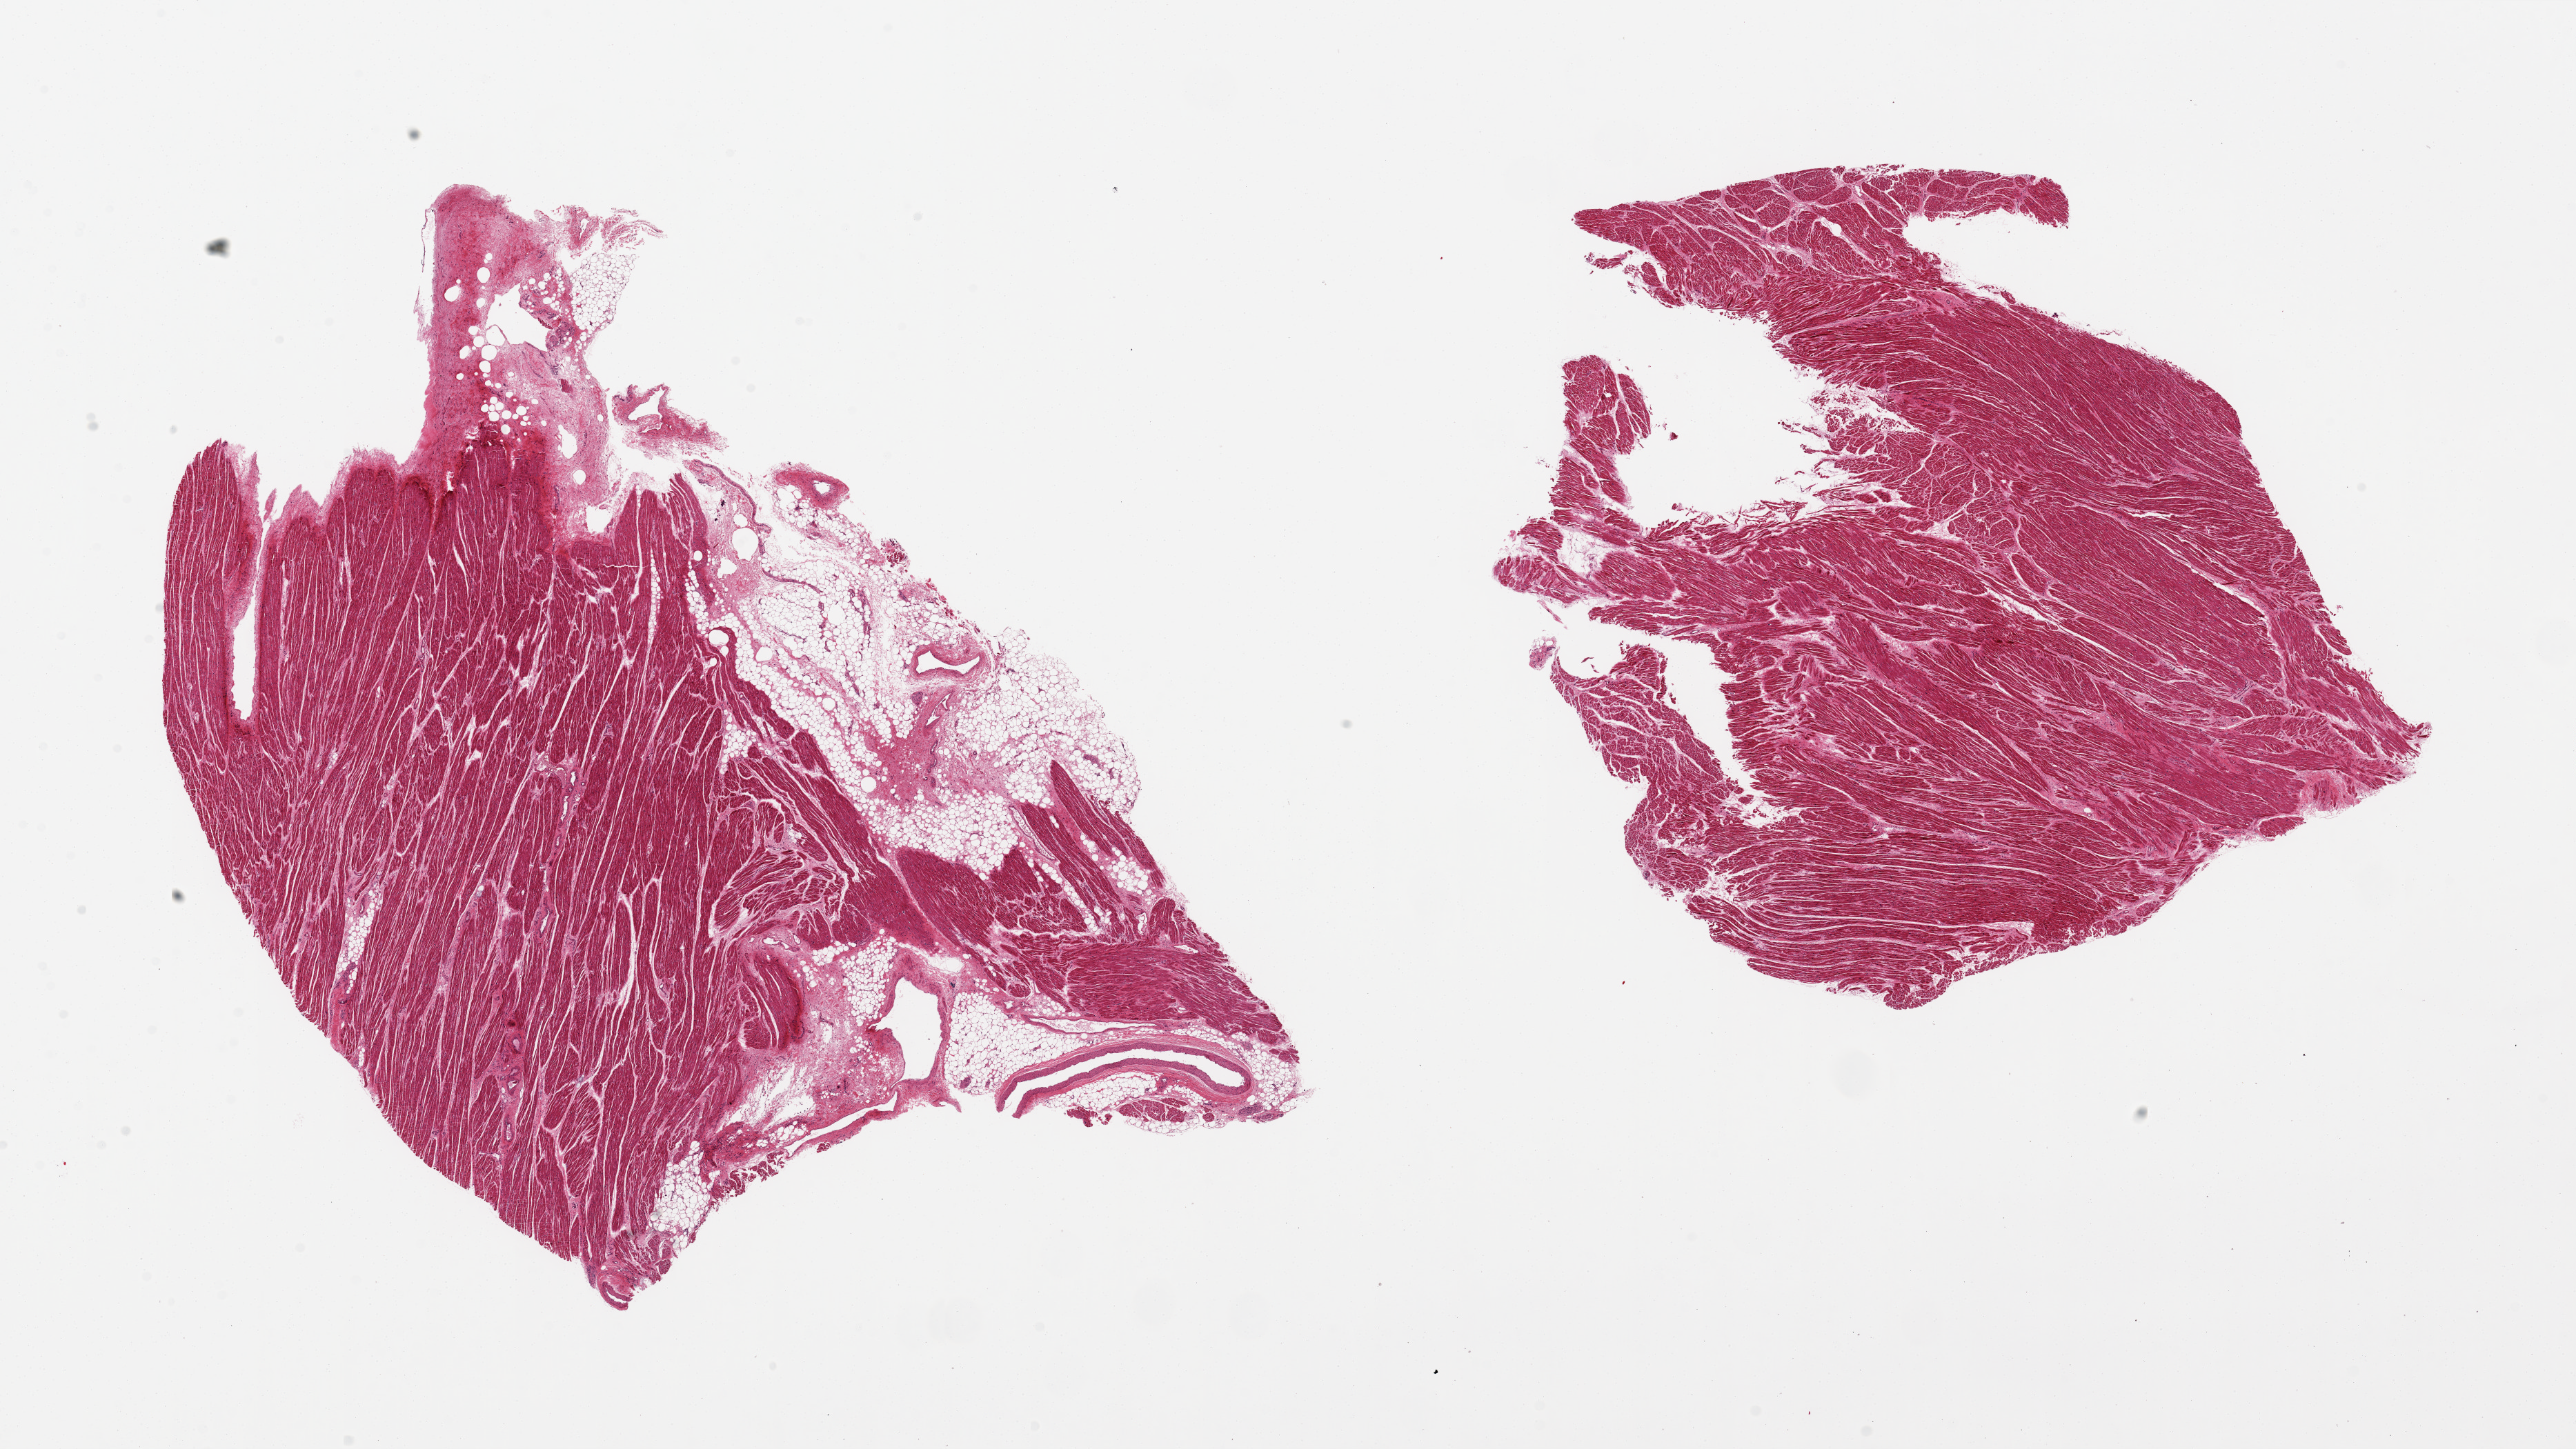
Whole-slide image, haematoxylin and eosin stain — low-resolution overview of the scanned area, about 29.5 x 16.6 mm (acquisition: 20x scan); PAXgene-fixed paraffin-embedded (PFPE) section; target tissue: auricular appendage; tissue donor sample. Donor: female.
Reviewer comment on this tissue sample: 2 pieces, 14.5x9 & 11.5x9mm. 1 well trimmed; 1 with 30% adipose.